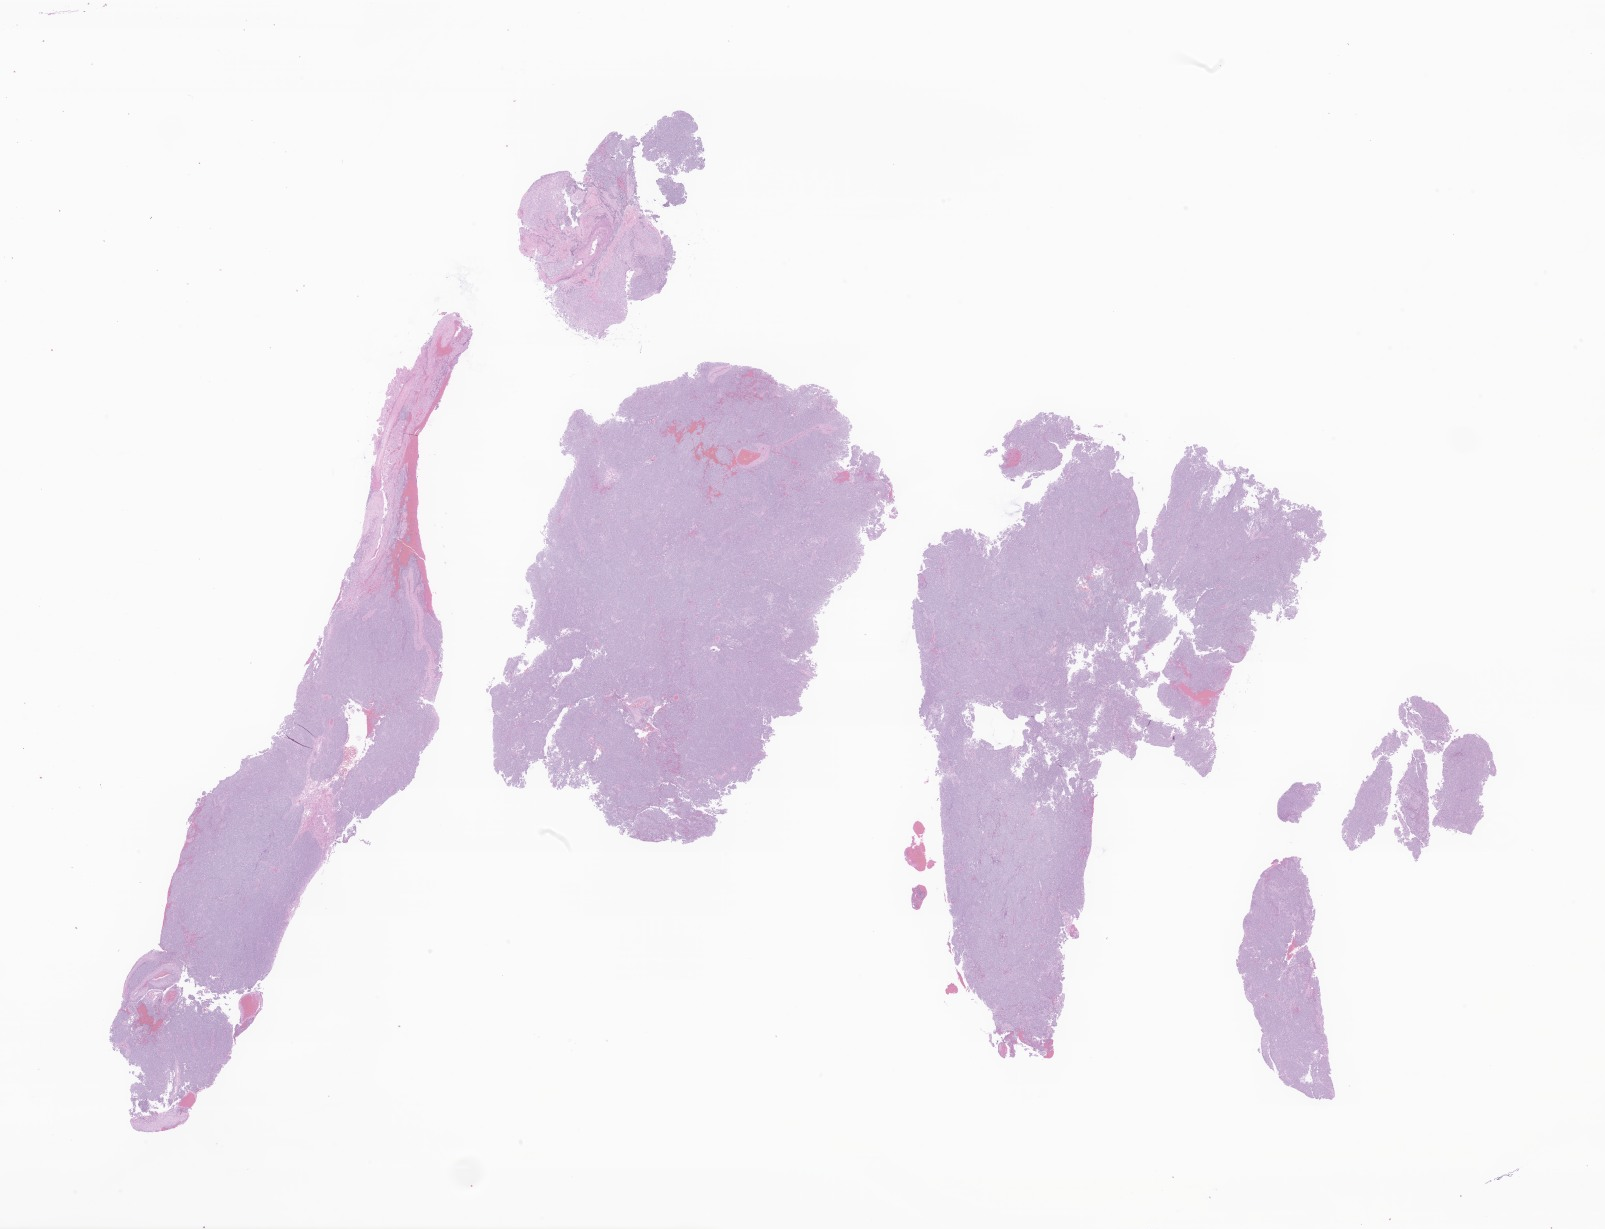
Whole-slide image, H&E stain of tumor tissue from the brain, whole scanned area (about 27.1 x 20.7 mm) shown as a low-resolution overview. Formalin-fixed, paraffin-embedded (FFPE) tissue. Patient female; age 131 months.
Diagnosis (ICD-O-3 morphology term): Medulloblastoma, NOS.